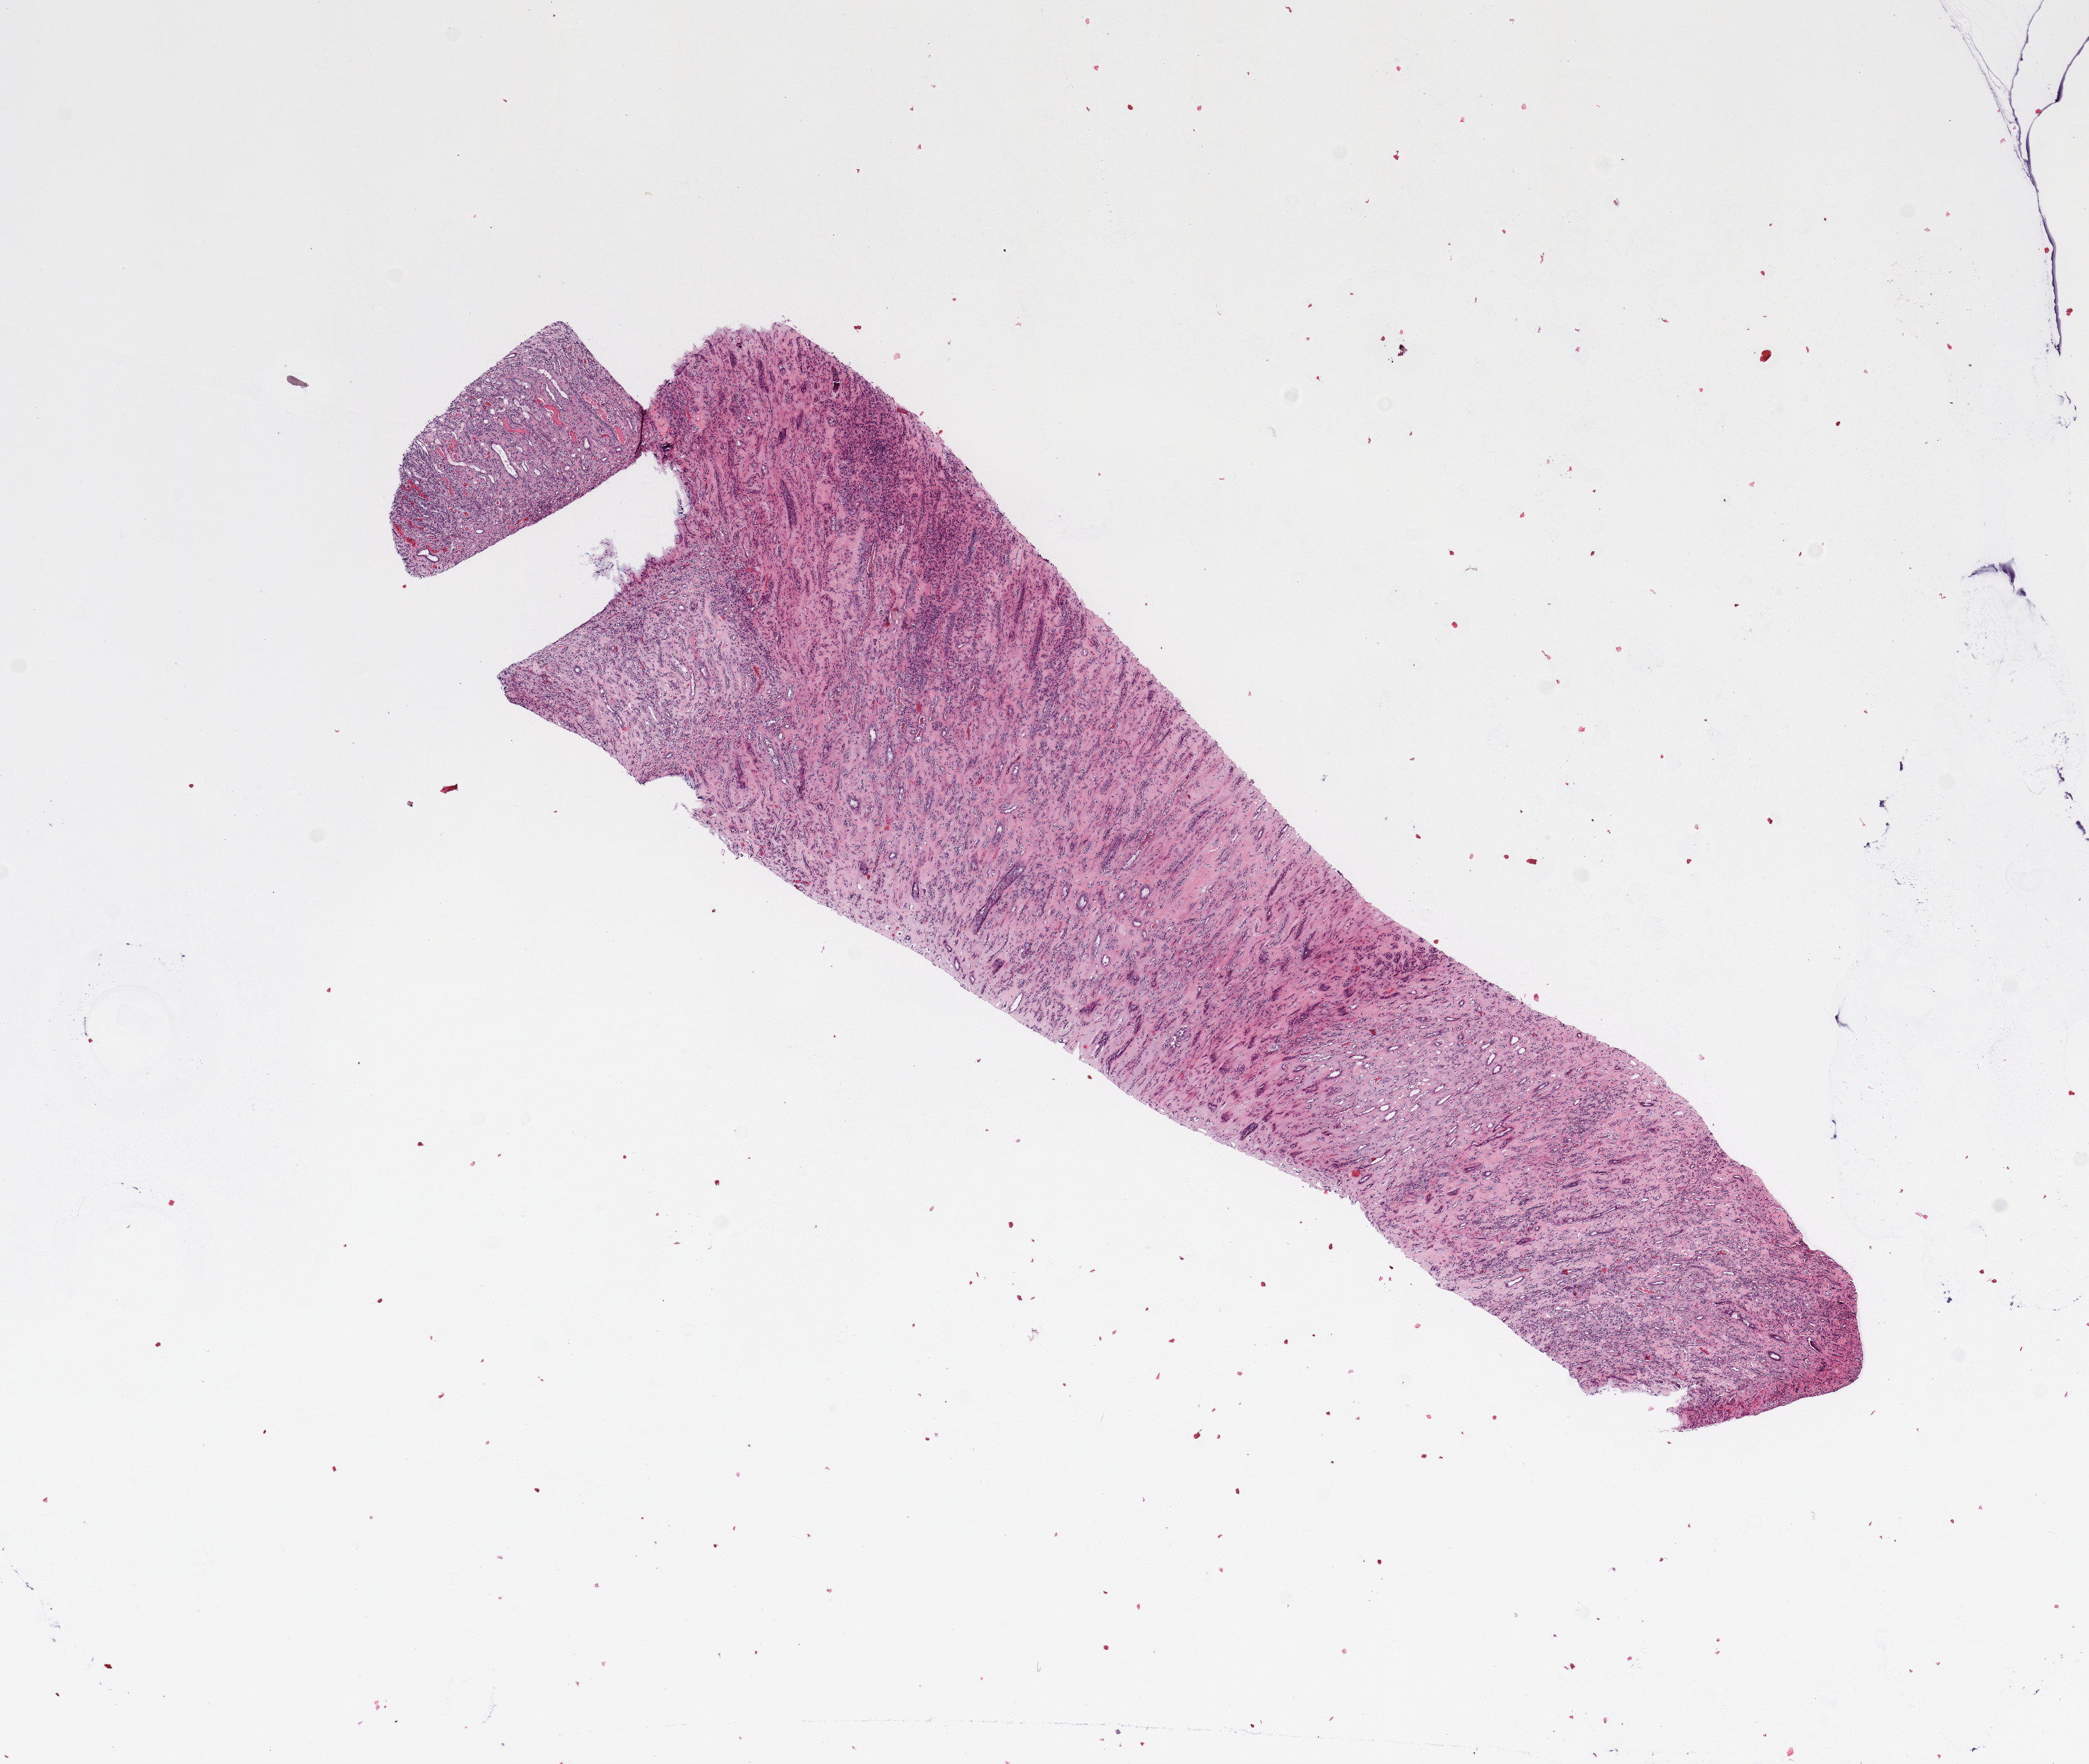
Digitized H&E-stained tissue section (whole slide), a low-resolution overview of the entire scanned area, about 11.8 x 10.0 mm (slide scanned at 20x), normal (non-tumour) tissue sample, sampled site: kidney. 47-year-old male patient.
This section: normal (non-tumour) tissue from the same patient. Patient diagnosis: Renal cell carcinoma, NOS.